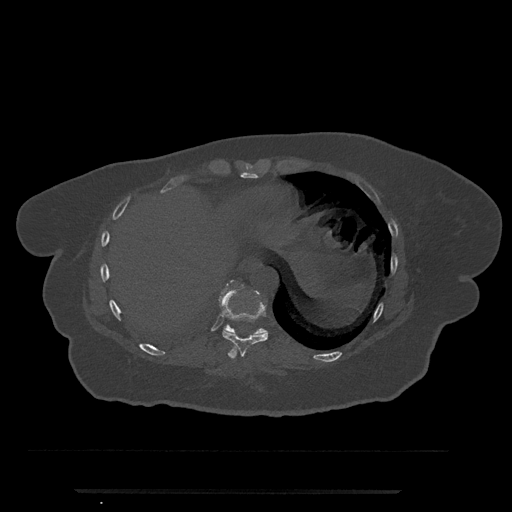
CT including the spine, one axial slice. Slice 325 of 797 in the series (ordered by position). Reconstruction kernel Br40s/3. 120 kVp. Bone window (W 1800 / L 400 HU). 0.5 mm slice thickness. 512 × 512 image matrix. Patient: female, 51 years. From the clinical record (not read from this slice): primary cancer: neuro.
Outlined on this slice (semi-automatic segmentation, software-assisted and operator-edited):
- T10 vertebra: bounding box (x1, y1, x2, y2) in pixels: (223, 281, 265, 336)
- T9 vertebra: (220, 283, 268, 358)